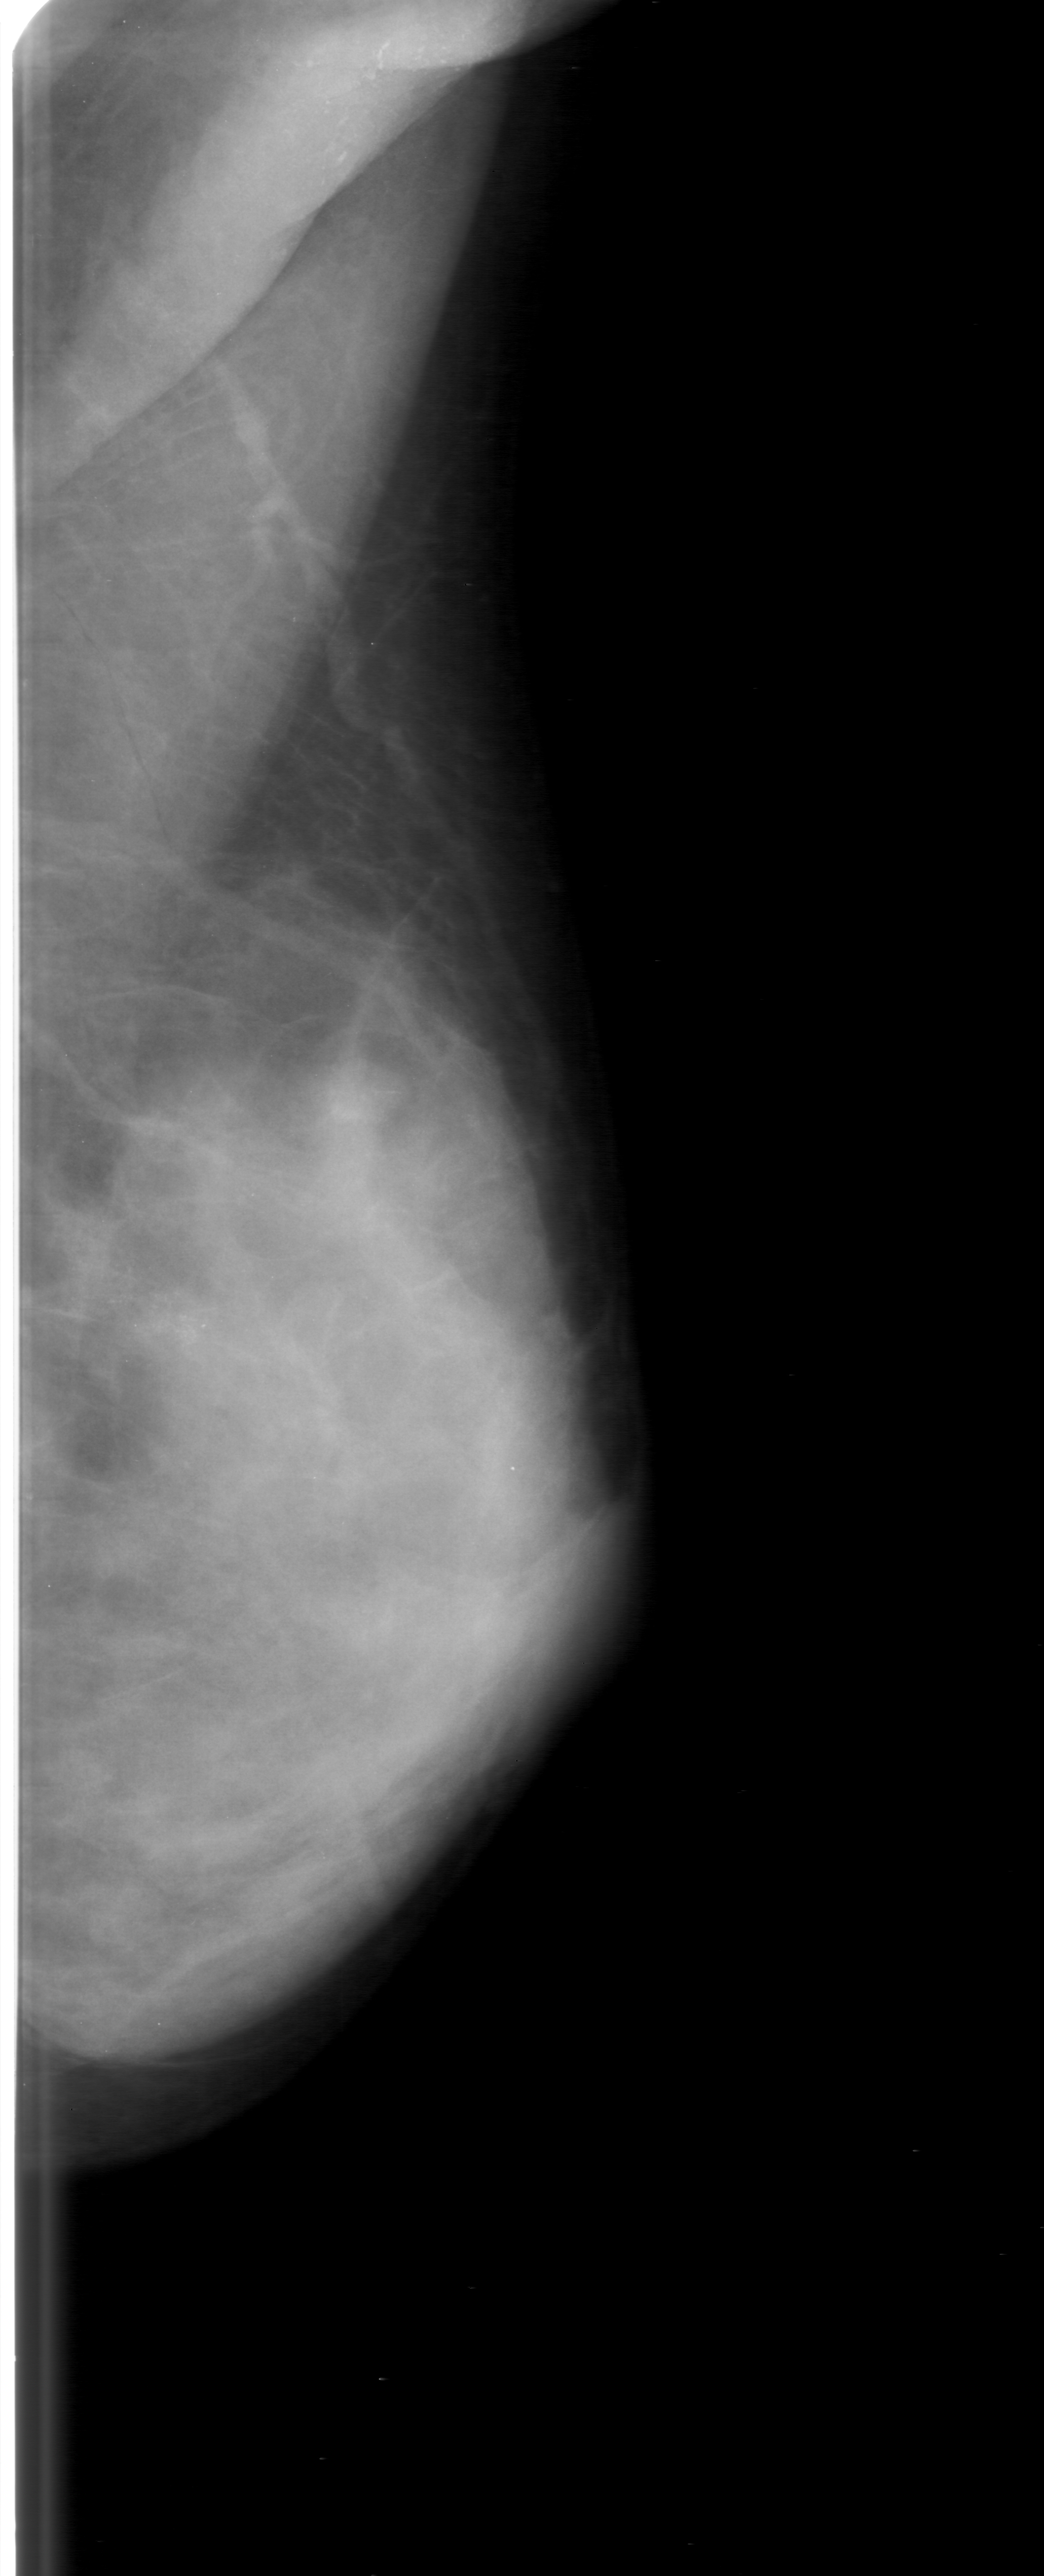
Mammogram (digitized film); left breast; mediolateral oblique (MLO) view; BI-RADS breast density category 3 (scale 1–4).
- Marked abnormality: calcifications, morphology fine linear branching, distribution linear; BI-RADS assessment category 3; subtlety rating 3 on a 1 (subtle) to 5 (obvious) scale; pathology (as recorded): malignant.